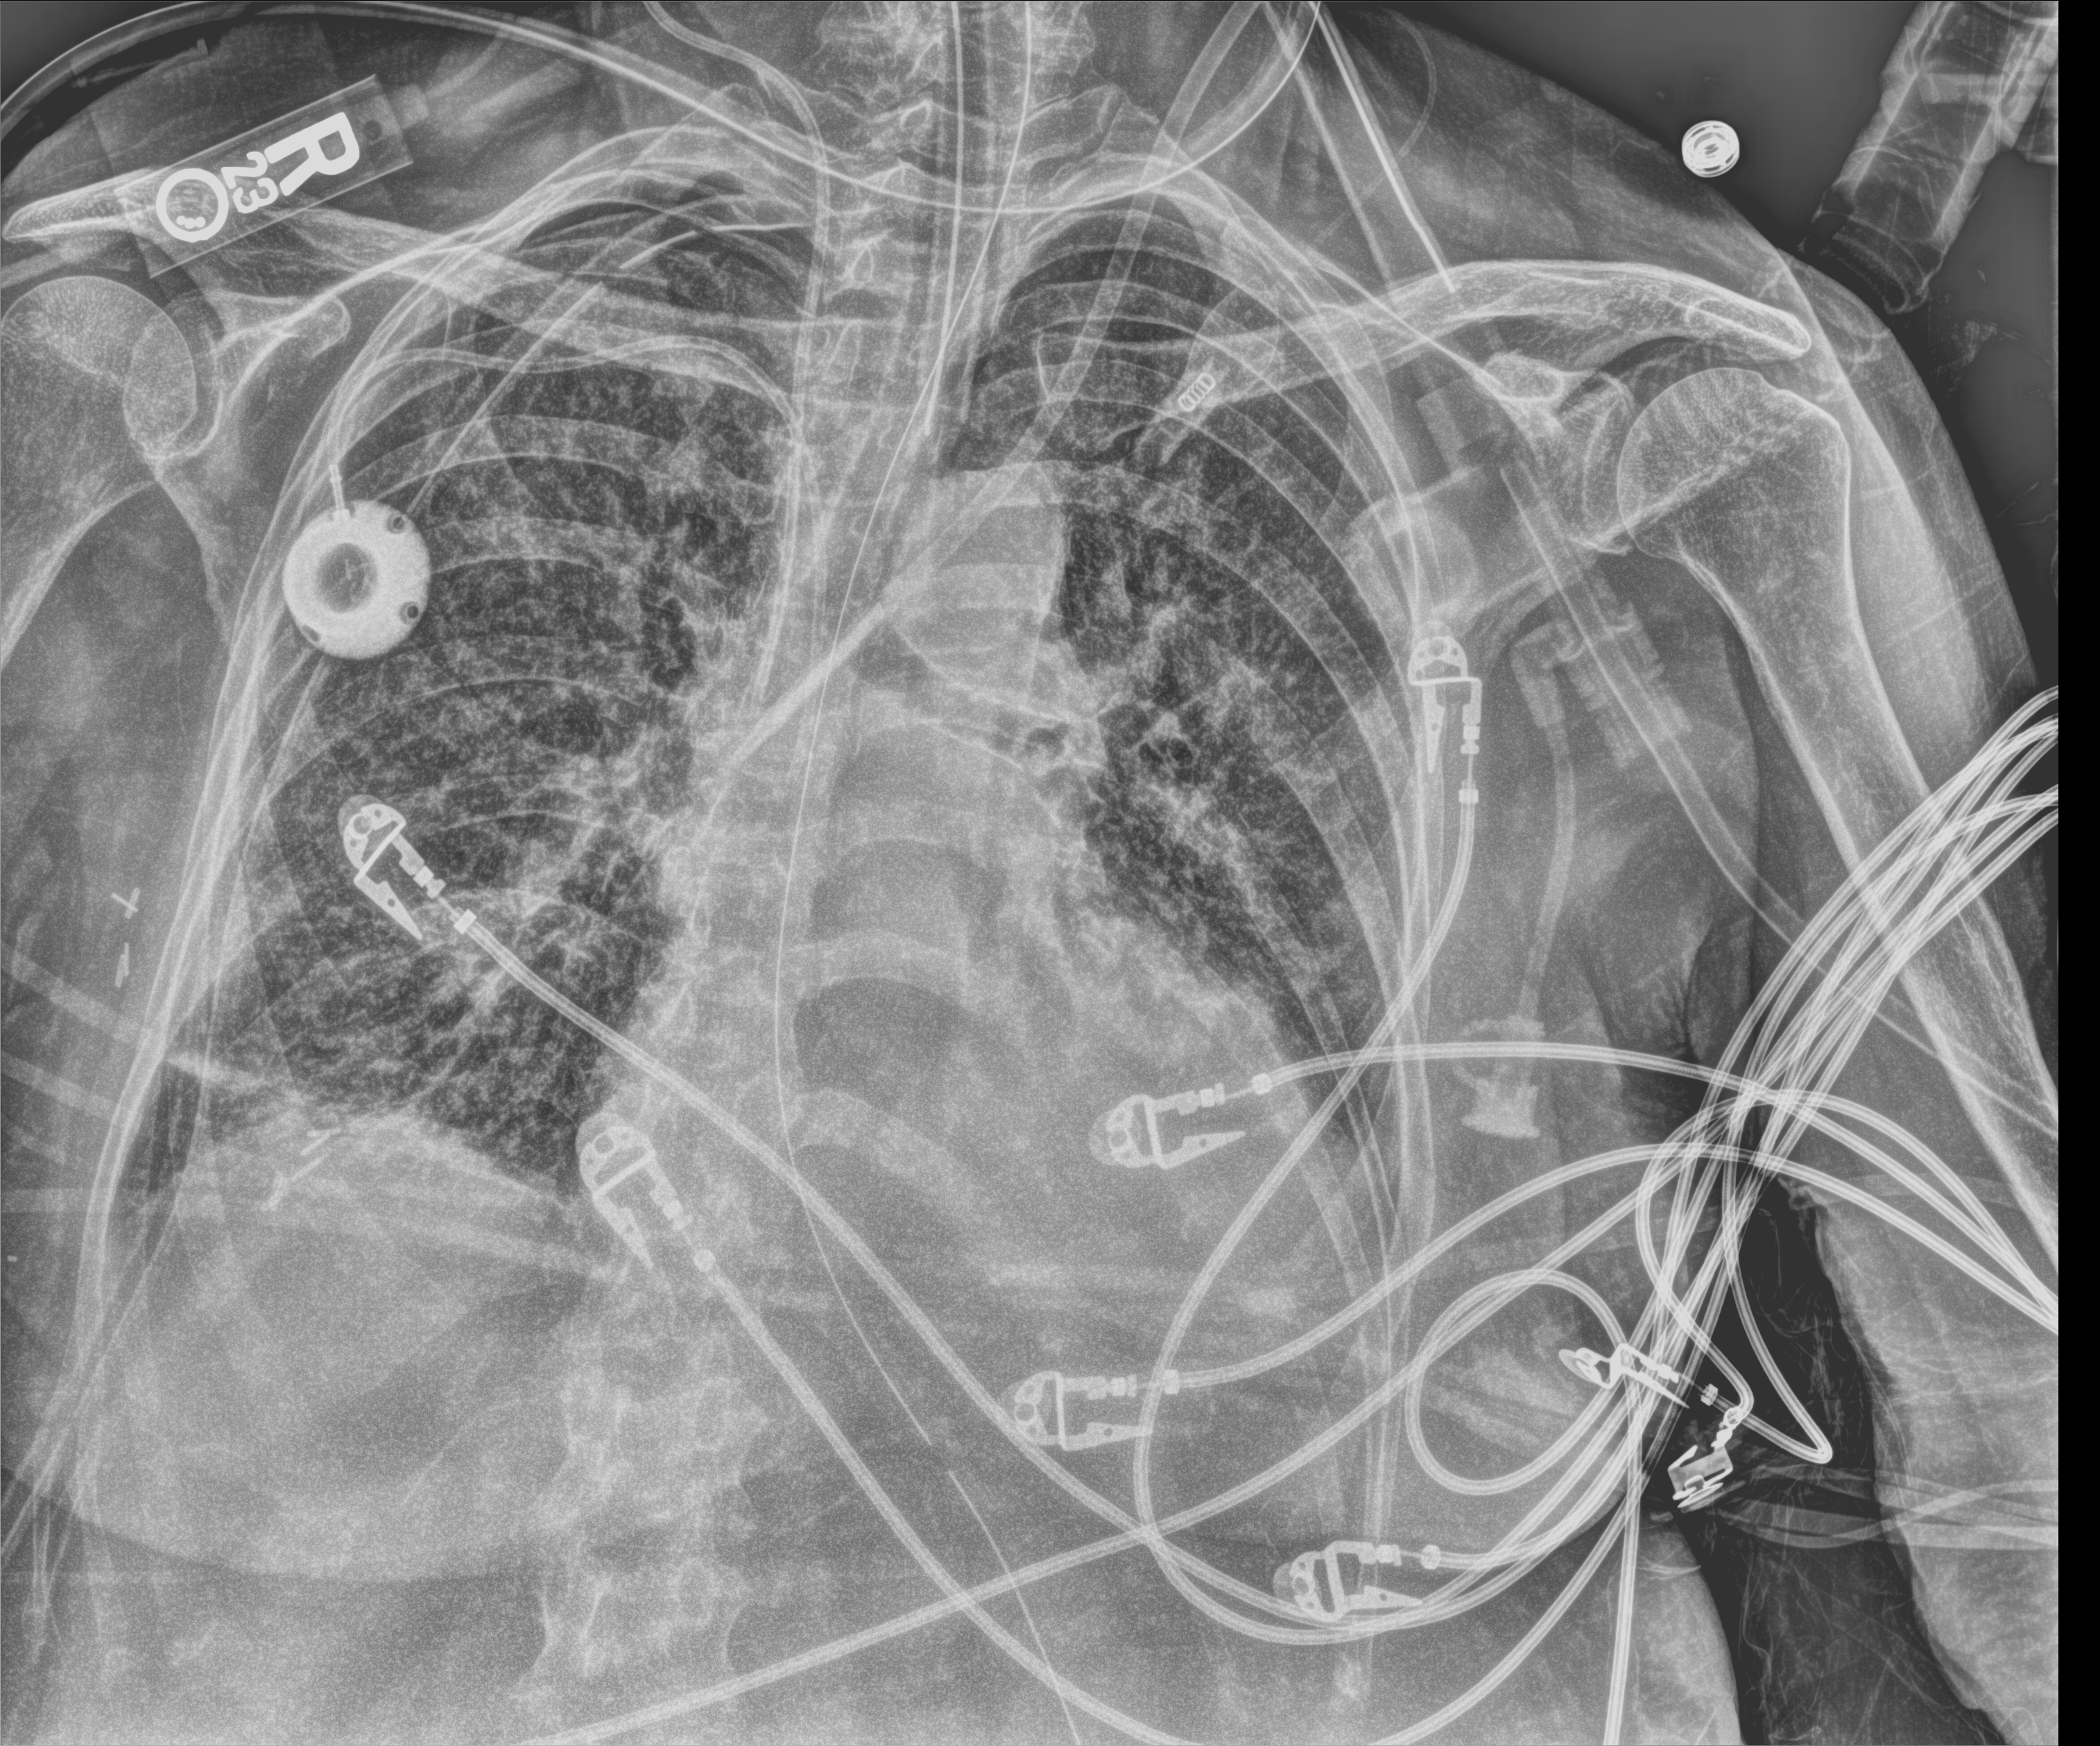
Chest X-ray (portable), anteroposterior (AP) projection. Patient hospitalised with COVID-19; female, aged 60–74 years.
Admission-level facts for this patient (not findings on this image; timing relative to this image not recorded): admitted to intensive care during this hospital stay: yes.